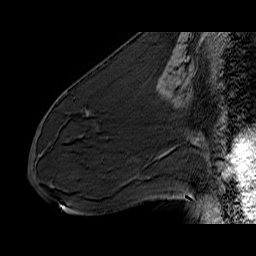
Breast MRI (dynamic contrast-enhanced), one sagittal slice. Position 30 of 60 along the scan axis. Dynamic contrast-enhanced series, time point 2 of 6 at this slice position (early post-contrast). 1.5 T. TE 6.5 ms, TR 32.9 ms. 256 × 256 image matrix, field of view 200 × 200 mm. Female patient. Case-level facts recorded for this patient, not image findings: setting: breast cancer imaged before/during neoadjuvant chemotherapy; receptor status: HER2-positive.
Outlined on this slice (semi-automatically segmented with operator editing):
- analysis volume of interest (the breast-tissue region the enhancement analysis was run in; not a lesion): bounding box [x1, y1, x2, y2] px = [72, 88, 133, 137]
- tumour enhancement mask (voxels above the 100 % enhancement threshold inside the analysis volume of interest): [86, 111, 90, 116]